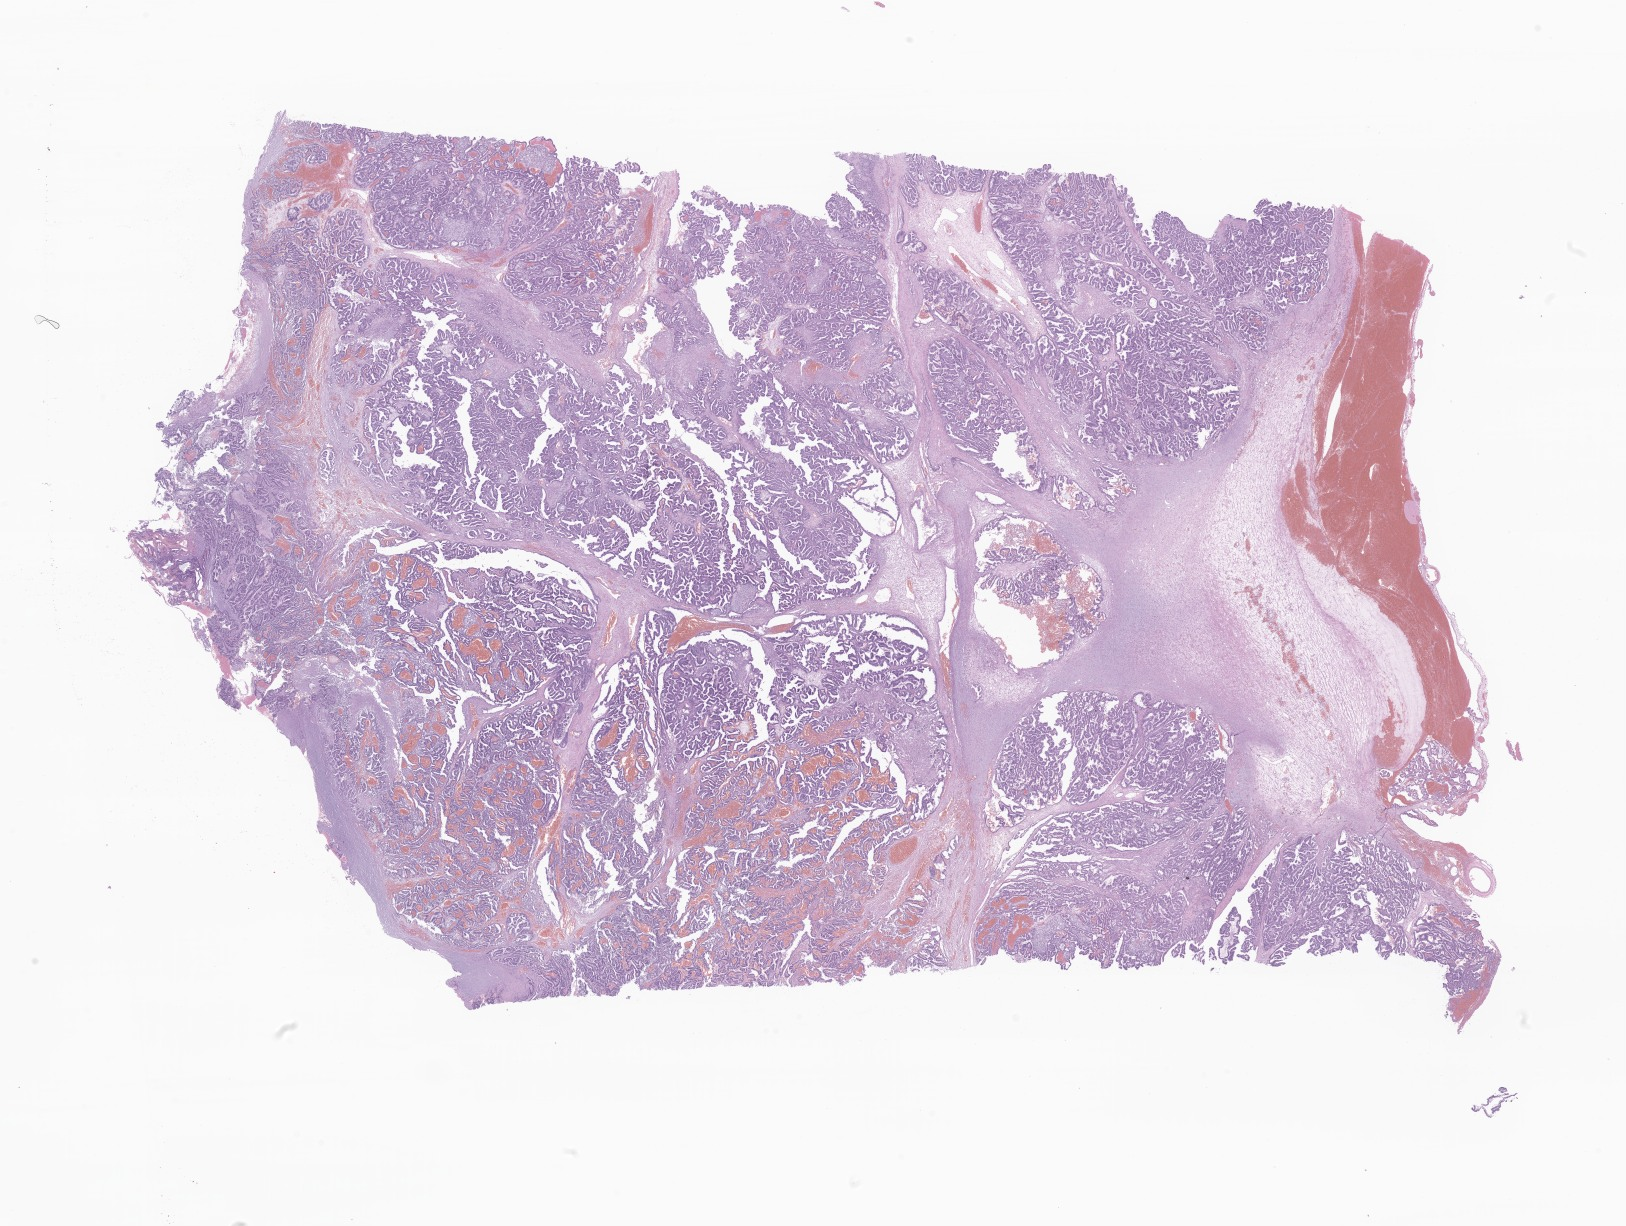
Whole-slide image, hematoxylin and eosin (H&E) stain of tumor tissue from the brain, shown as a low-resolution overview of the whole scanned area (about 27.4 x 20.7 mm). Formalin-fixed paraffin-embedded section. Patient female; age 67 days.
Diagnosis: Neoplasm, uncertain whether benign or malignant.